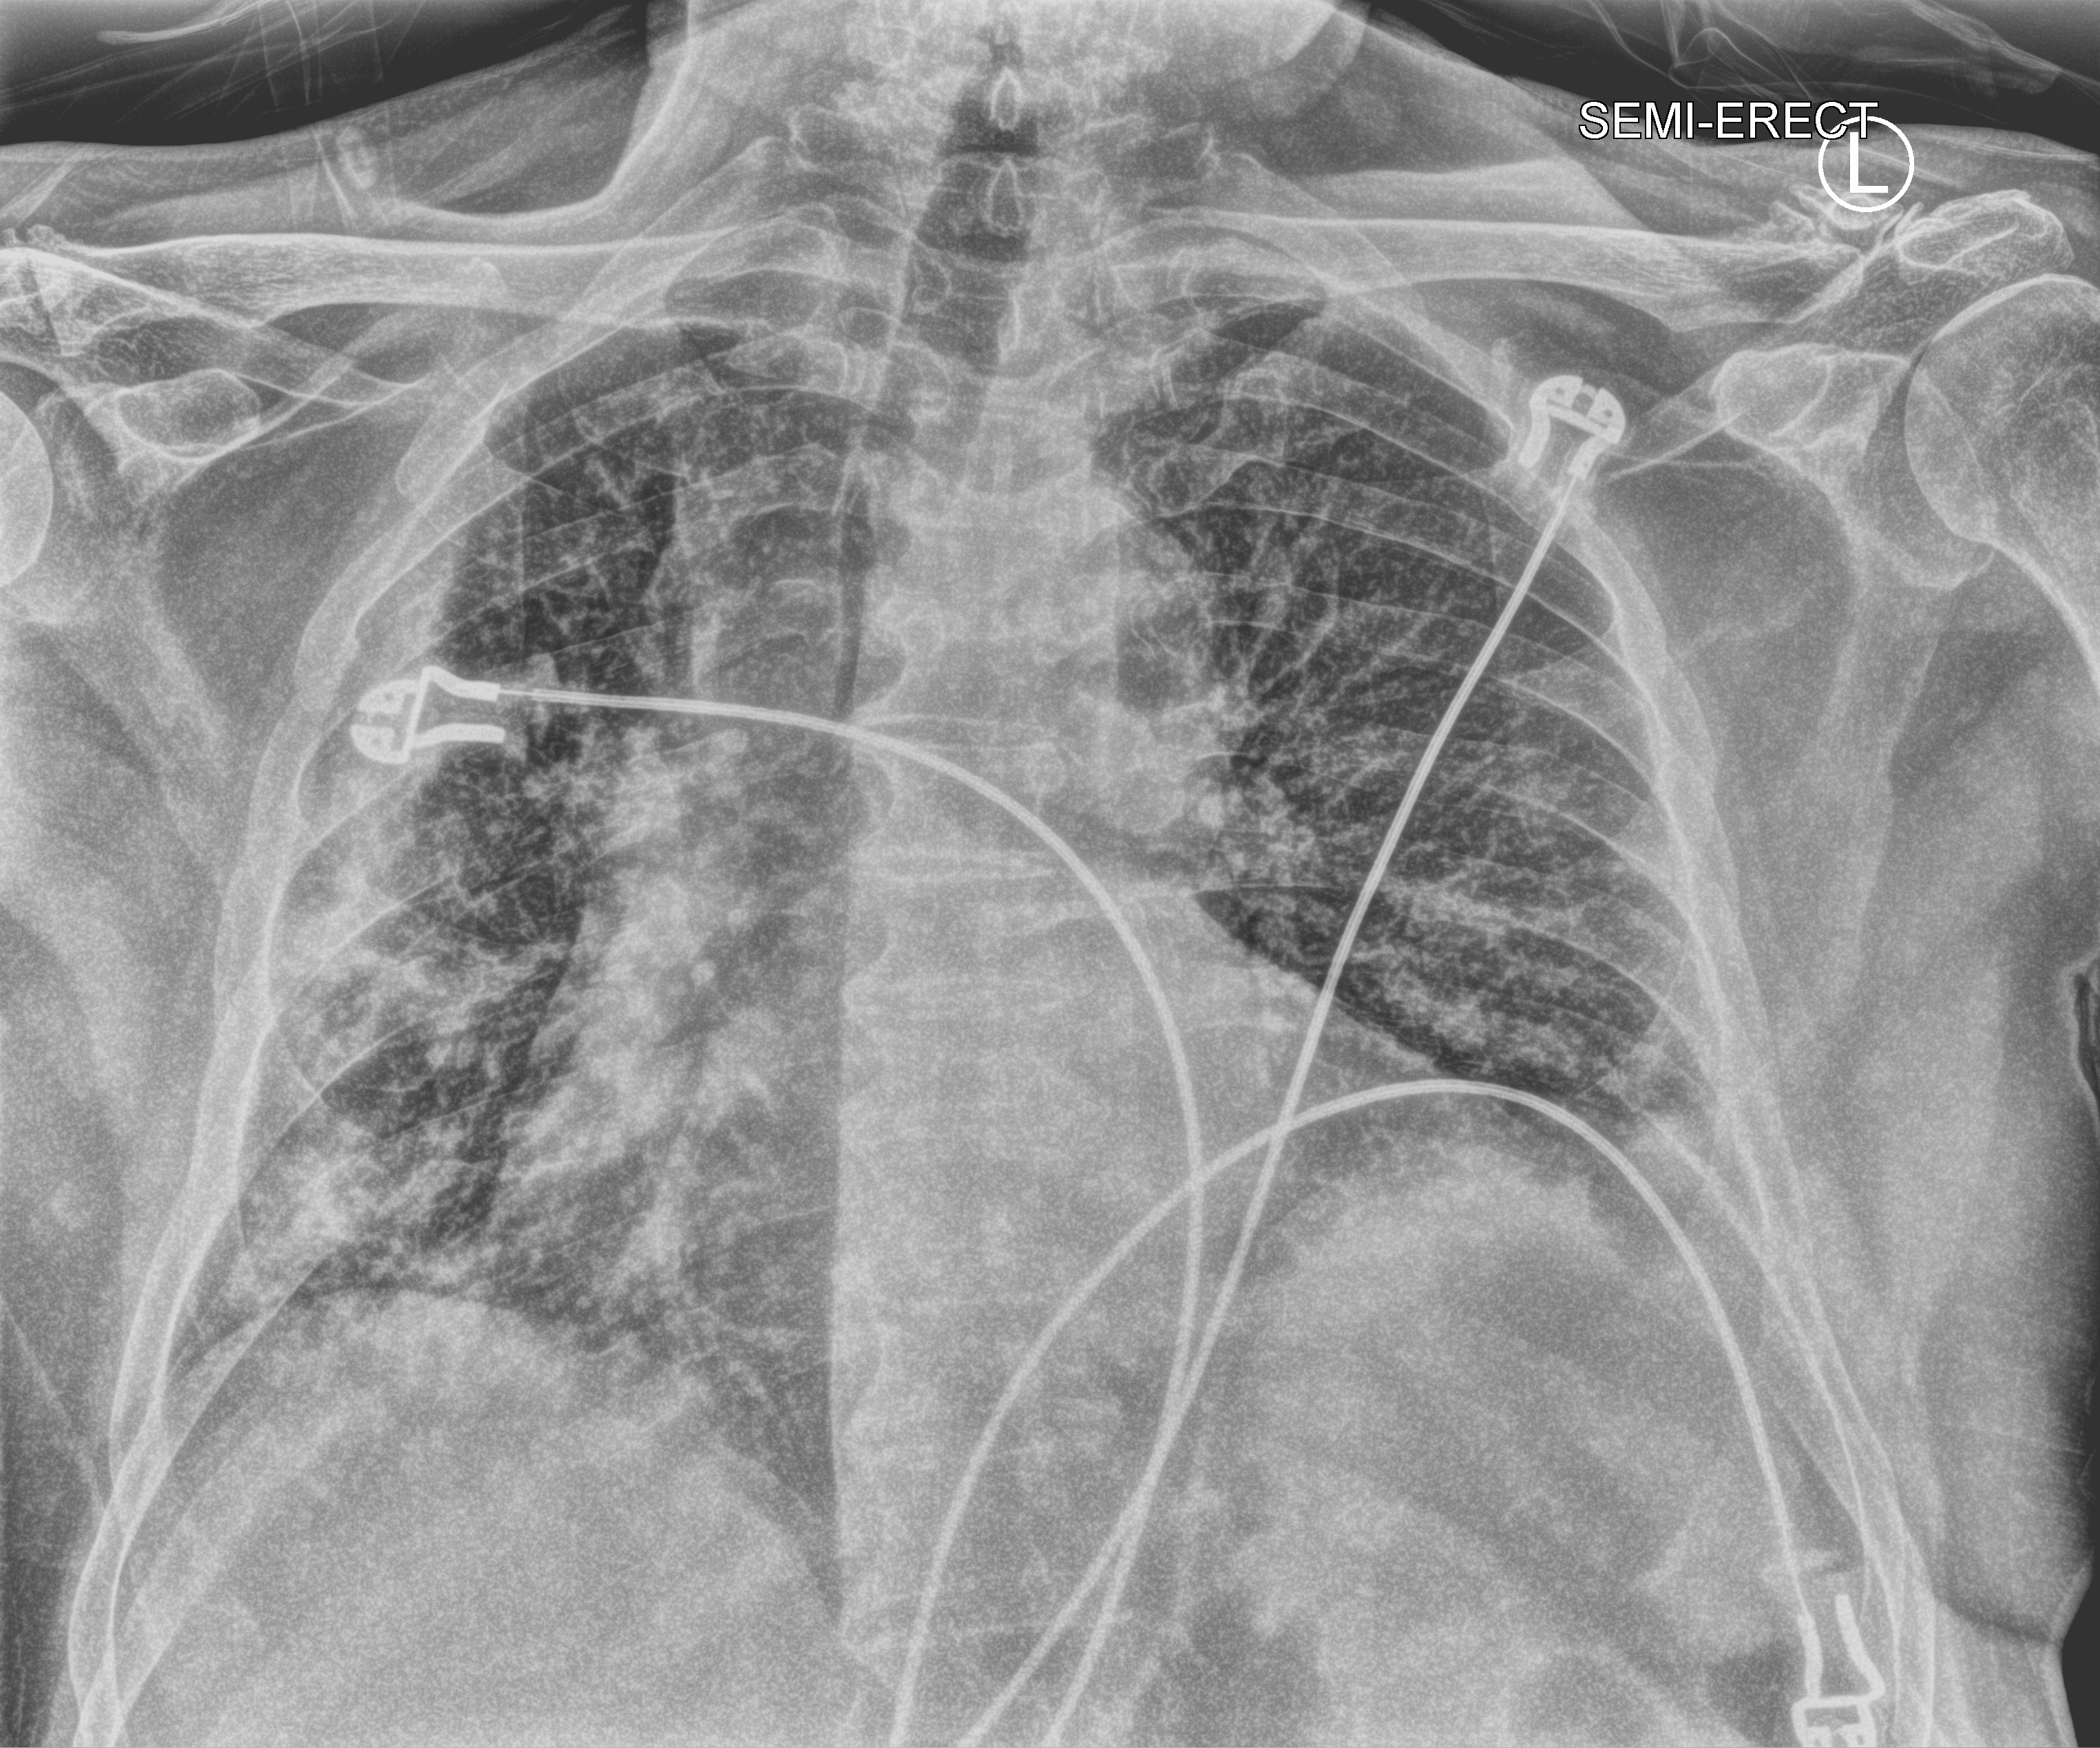
Chest X-ray (portable), anteroposterior (AP) projection. Male patient hospitalised with COVID-19, age 75–90 years.
From the hospital-stay record, not from the radiograph (when in the stay this image was taken is not recorded):
- admitted to intensive care during this hospital stay: no
- mechanically ventilated during this hospital stay: no